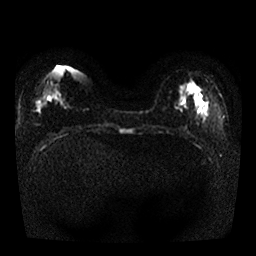
Breast MRI, one axial slice; position 12 of 25 along the scan axis; diffusion-weighted series; image 2 of 4 stored at this slice position (different b-values; order by instance number); 1.5 T; 4 mm slice thickness; 256 × 256 image matrix. Female patient.
Structures marked on this image (expert manual segmentation):
- tumour on diffusion-weighted imaging: bounding box (x1, y1, x2, y2) in pixels: (194, 88, 200, 96)